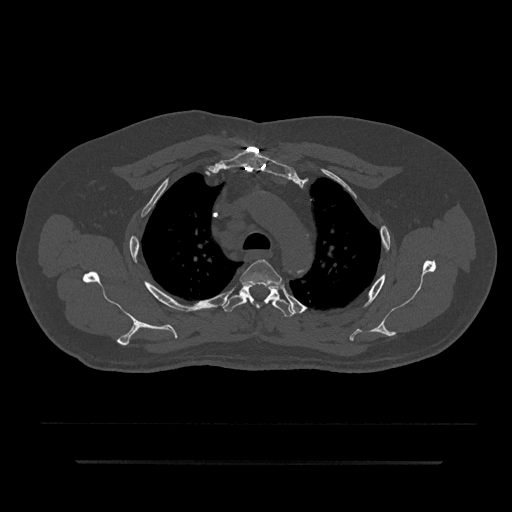
CT including the spine, one axial slice; slice 635 of 797 in the series (ordered by position); reconstruction kernel Br40s/3; bone window (W 1800 / L 400 HU); 0.5 mm slice thickness; 512 × 512 image matrix, field of view 464 × 464 mm. Patient: male, 59 years. From the clinical record (not read from this slice): primary cancer: bile ducts; vertebrae with lytic lesions (as recorded): T10.
Structures marked on this image (semi-automatically segmented with operator editing):
- T3 vertebra: bounding box (x1, y1, x2, y2) in pixels: (240, 259, 282, 287)
- T4 vertebra: (222, 283, 294, 317)